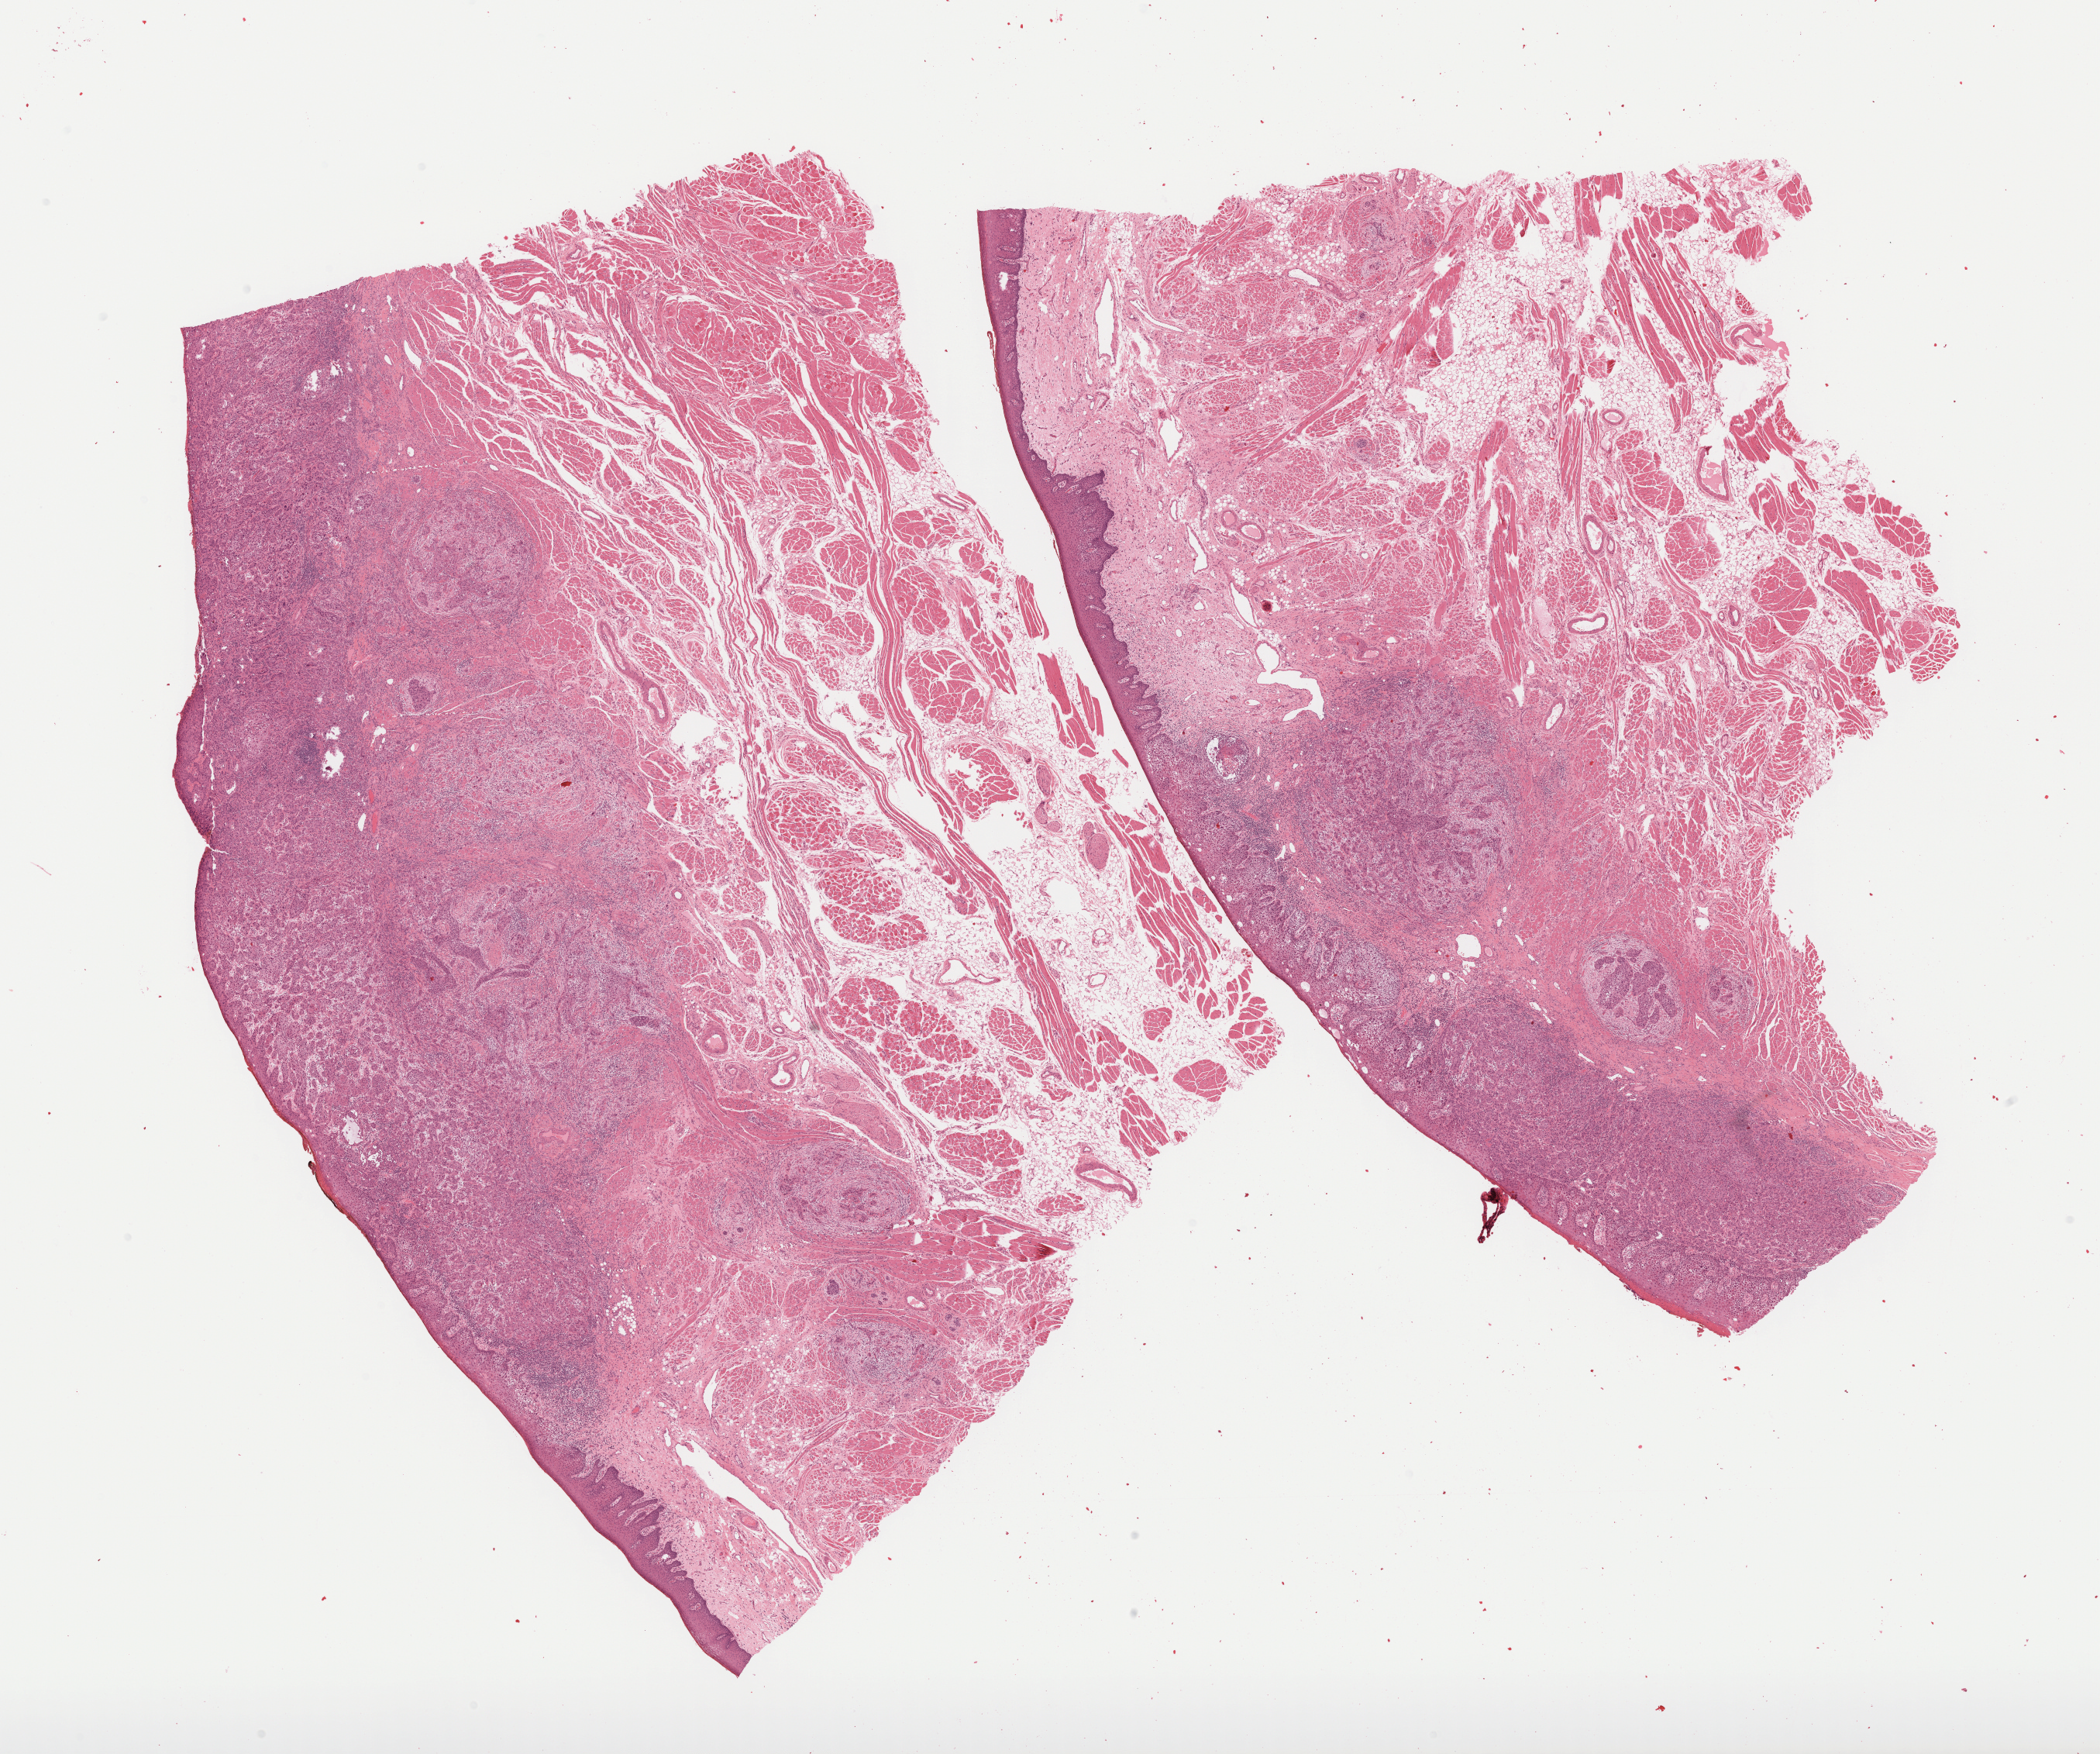
H&E whole-slide image, shown as a low-resolution overview of the whole scanned area (about 21.8 x 18.2 mm), formalin-fixed paraffin-embedded (FFPE) diagnostic section, primary tumour sample from the head and neck. Patient: female, age at initial diagnosis 75 years. Histologic grade: G3 (poorly differentiated).
* pathologic diagnosis: Squamous cell carcinoma, NOS (mouth, NOS)
* AJCC pathologic stage: I
* TNM: T1 N0
* laterality: left
* lymph nodes positive (case pathology): 0 of 15 examined